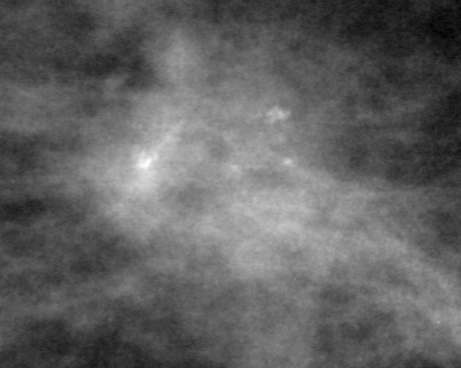
Region of interest cut from a scanned film mammogram (one marked finding); left breast; MLO view; BI-RADS breast density category 2 (scale 1–4).
Marked abnormality: mass, shape asymmetric breast tissue, margins ill defined; BI-RADS assessment category 4; pathology result (as recorded, not read from the image): malignant.